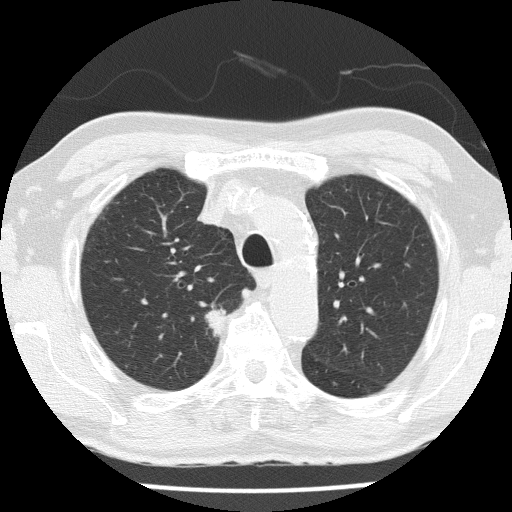
Low-dose screening chest CT, axial slice, third annual screen, lung window (W 1500 / L -600 HU), 2 mm slice thickness, lung (sharp) reconstruction kernel (FC51), 120 kVp, slice 43 of 153 in the series. Male participant, aged 72 years at enrolment. Current smoker at enrolment.
Lesion marked by an expert reader, bounding box (x1, y1, x2, y2) in pixels: (187, 296, 239, 347). Reader record for this screening exam (exam-level; its link to the box is not recorded): non-calcified nodule or mass ≥4 mm, right upper lobe, 14 × 14 mm, spiculated (stellate) margins, soft tissue attenuation, pre-existing on the prior screen: yes; interval growth: yes. Official screen result: positive, other. Participant outcome: lung cancer diagnosed 67 days after this screen — squamous cell carcinoma, NOS, right upper lobe, moderately differentiated (G2), stage IIA (AJCC 6th edition), 25 mm at pathology.